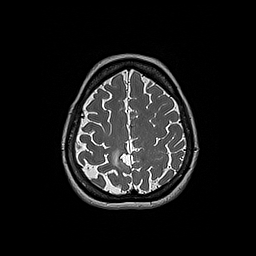
Brain MRI from a brain-tumour surgery series, one axial slice. Slice 54 of 192 in the series (ordered by position). 256 × 256 image matrix, field of view 250 × 250 mm. Case-level facts recorded for this patient, not image findings: histopathology: Oligodendroglioma; WHO grade: 2; IDH mutation: yes.
Outlined on this slice (outlined manually by an expert reader):
- tumour: bounding box (x1, y1, x2, y2) in pixels: (112, 149, 122, 170)